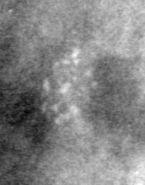
Cropped region of a digitized screen-film mammogram centred on a radiologist-marked abnormality; left breast; MLO view; BI-RADS breast density category 4 (scale 1–4).
Finding: calcifications, morphology pleomorphic, distribution clustered; BI-RADS assessment category 4; pathology (as recorded): benign.